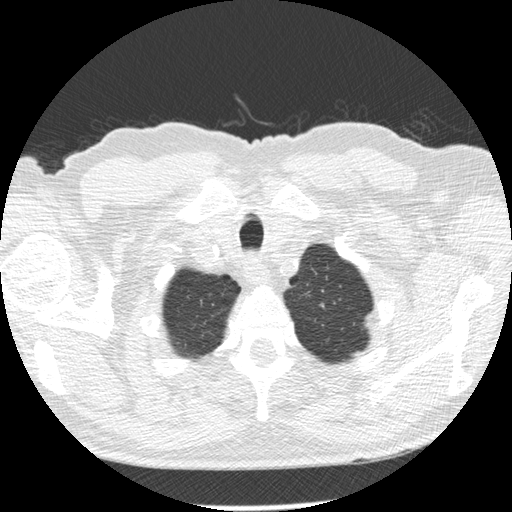
Low-dose screening chest CT, axial slice, second annual screen, lung window (W 1500 / L -600 HU), standard (soft-tissue) reconstruction kernel (STANDARD), 512 × 512 image matrix, field of view 360 × 360 mm. Male, age 73 years at enrolment.
Lesion marked by an expert reader, bounding box [x1, y1, x2, y2] px = [350, 304, 391, 347]. Screening reader's record for this exam: no non-calcified nodule ≥4 mm recorded. Participant outcome: lung cancer diagnosed 457 days after this screen — adenocarcinoma, NOS, left upper lobe, poorly differentiated (G3), stage IB (AJCC 6th edition), 10 mm at pathology.